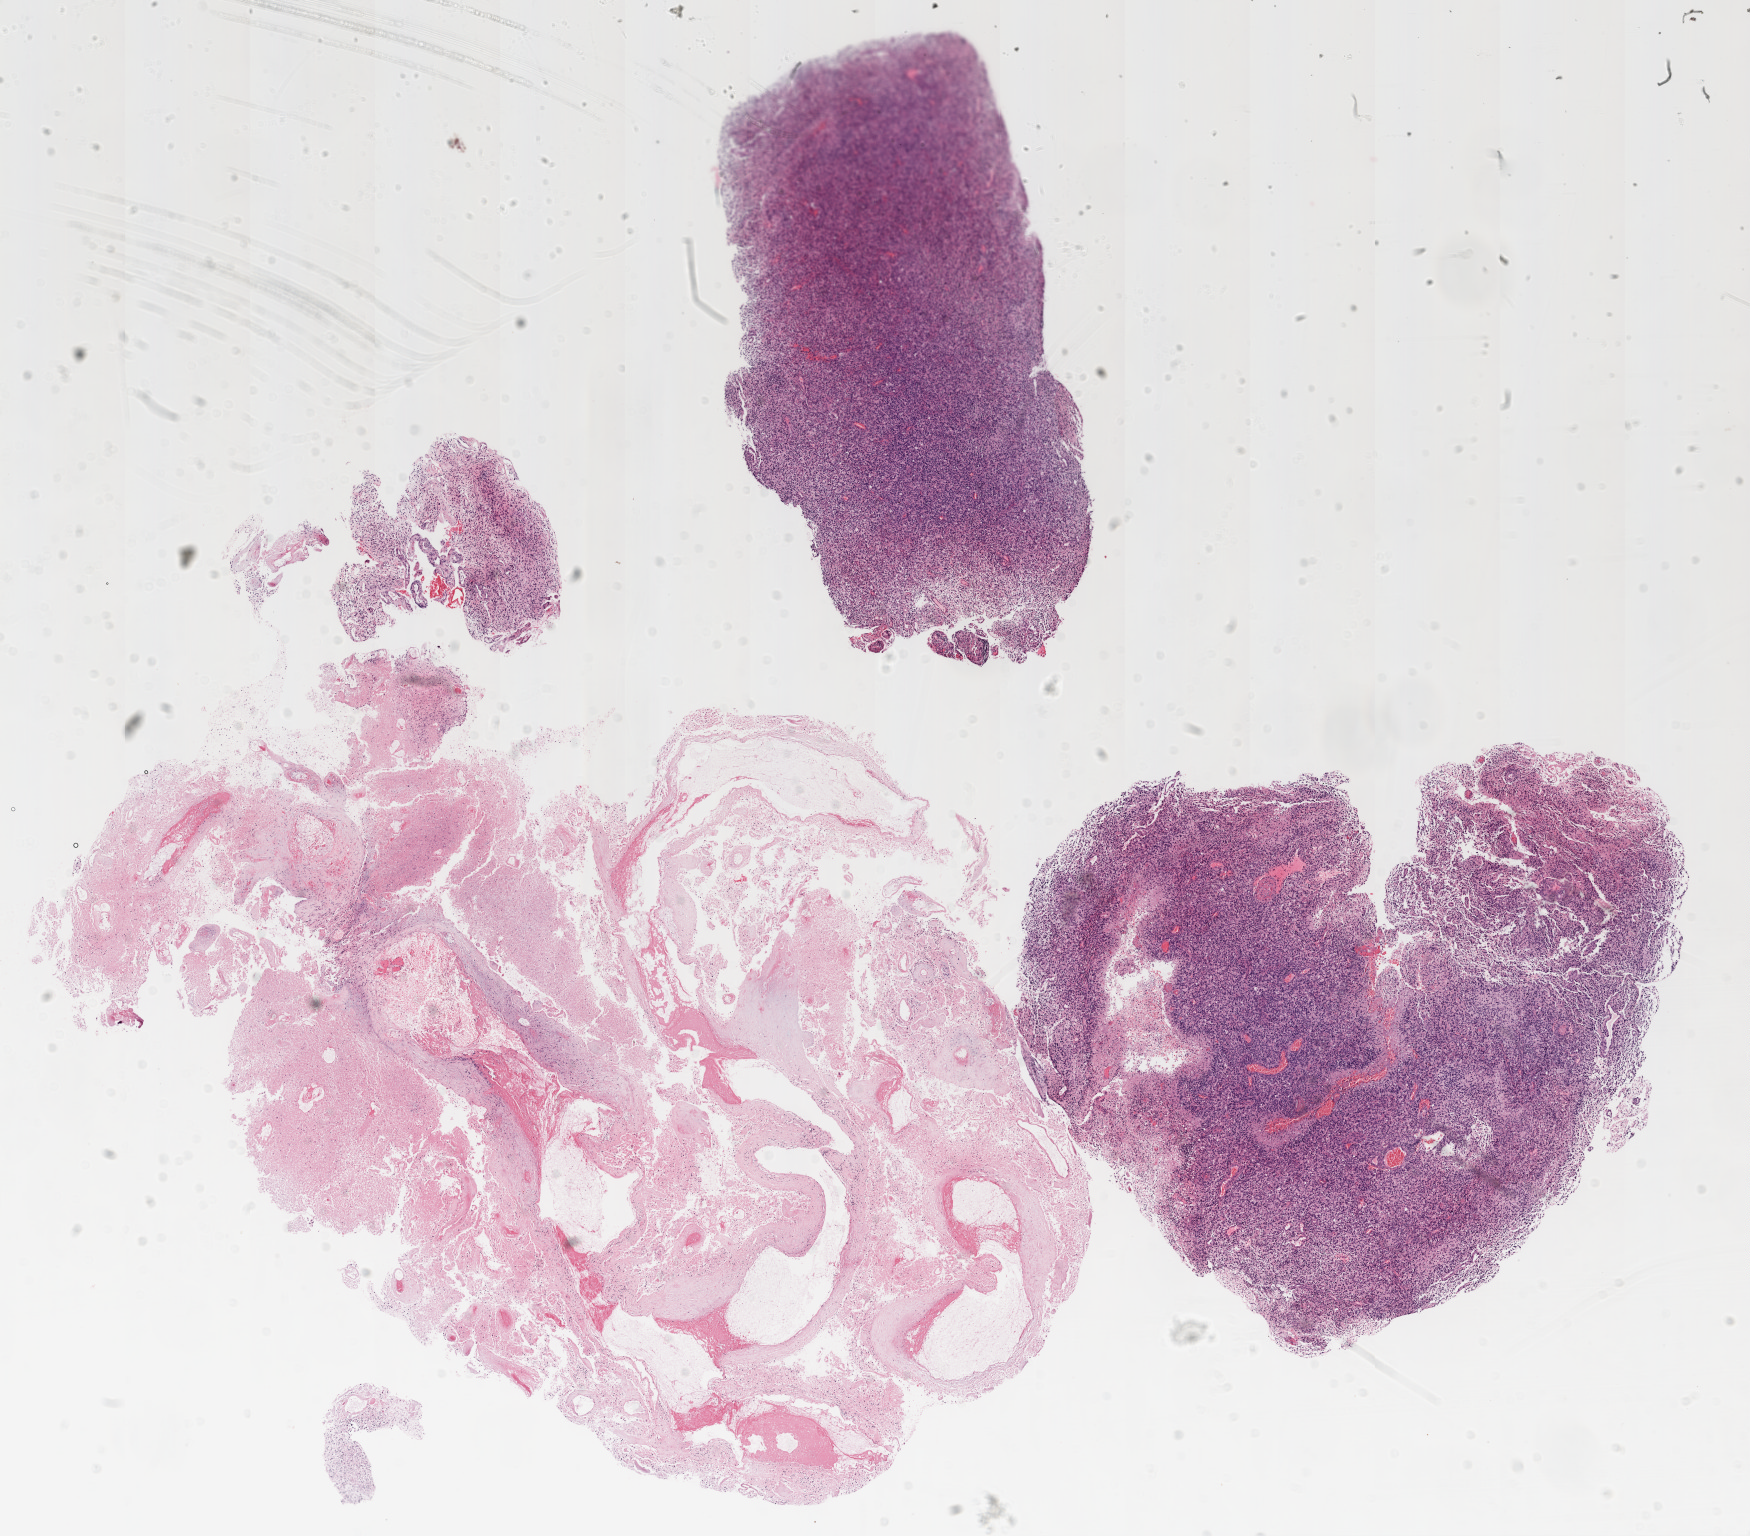
Digitized H&E-stained tissue section (whole slide) — shown as a low-resolution overview of the whole scanned area (about 14.0 x 12.3 mm, acquisition: 20x scan), FFPE section, brain, primary tumour sample. Male, age 60 years at initial diagnosis.
Diagnosis: Glioblastoma.